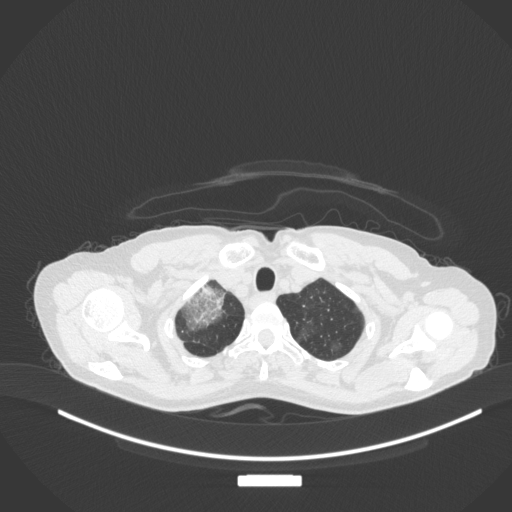
Chest CT, one axial slice; position 295 of 311 along the scan axis; reconstruction kernel B31f; 120 kVp; lung window (W 1500 / L -600 HU); 512 × 512 image matrix, field of view 400 × 400 mm. Female patient, age 59 years. From the clinical record (not read from this slice): clinical TNM (as recorded): T3 N0 M0; histopathological grade: G1.
Structures marked on this image (rectangle marked by the reading radiologist):
- lung tumour (recorded histology: adenocarcinoma): bounding box (x1, y1, x2, y2) in pixels: (174, 278, 232, 331)